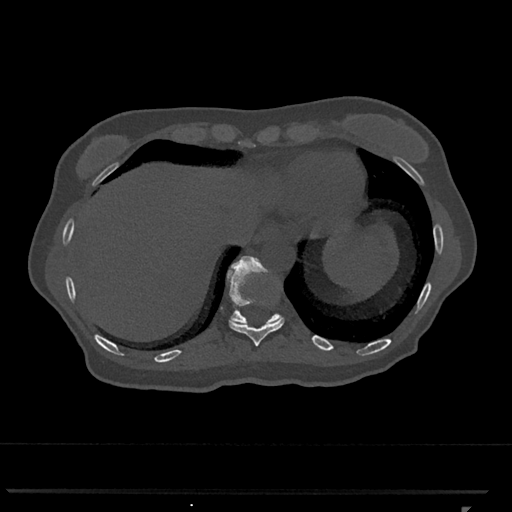
CT including the spine, one axial slice. Position 554 of 793 along the scan axis. Reconstruction kernel Br40s/3. 120 kVp. Bone window (W 1800 / L 400 HU). 512 × 512 image matrix, field of view 380 × 380 mm. Female patient, age 62 years. Case-level facts recorded for this patient, not image findings: primary cancer: renal.
Annotated regions visible in this slice (semi-automatically segmented with operator editing):
- T10 vertebra: box from (x=229, y=274) to (x=285, y=346) px
- T11 vertebra: (x=227, y=256)–(x=283, y=325)